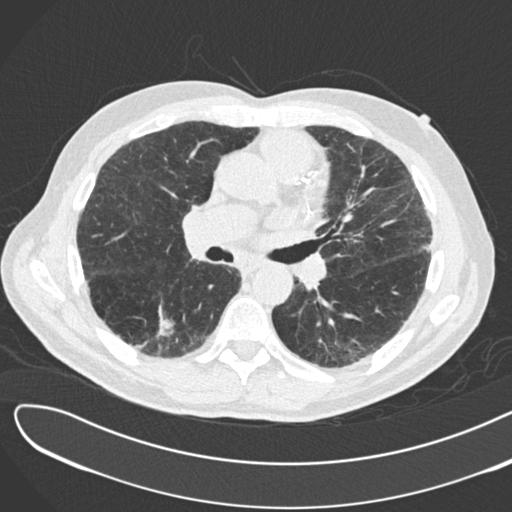
Low-dose screening chest CT, one axial slice; slice 94 of 183 in the series (ordered by position); reconstruction kernel B30f; 120 kVp; lung window (W 1500 / L -600 HU); 2 mm slice thickness; 512 × 512 image matrix.
Outlined on this slice (manually delineated by an expert):
- lesion 1 (tumor, lower lobe of right lung): bounding box <158,319,174,335> (left, top, right, bottom; pixels)